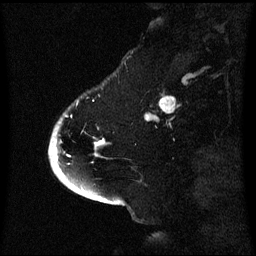
Breast MRI (dynamic contrast-enhanced), one sagittal slice; position 14 of 60 along the scan axis; dynamic contrast-enhanced series, image 2 of 3 at this slice position (ordered by acquisition); 1.5 T; TE 4.2 ms, TR 8.4 ms; 256 × 256 image matrix. Female patient, age 53 years. From the clinical record (not read from this slice): setting: breast cancer imaged before/during neoadjuvant chemotherapy; receptor status: HR-positive, HER2-negative.
Structures marked on this image (semi-automatically segmented with operator editing):
- analysis volume of interest (the breast-tissue region the enhancement analysis was run in; not a lesion): bounding box [x1, y1, x2, y2] px = [52, 116, 109, 171]
- tumour enhancement mask (voxels above the 70 % enhancement threshold inside the analysis volume of interest): [55, 140, 105, 159]